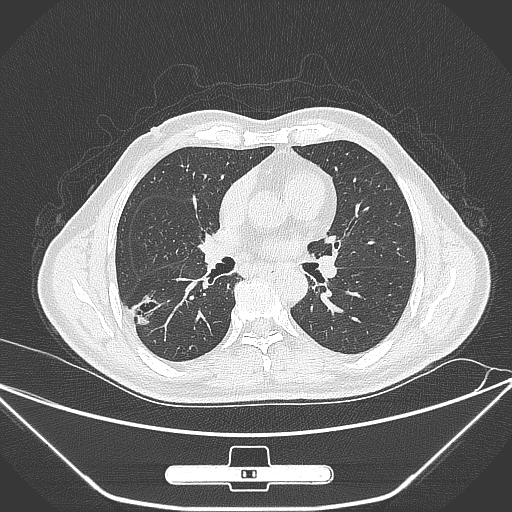
Chest CT, one axial slice; position 151 of 310 along the scan axis; lung window (W 1500 / L -600 HU); 1 mm slice thickness; 512 × 512 image matrix, field of view 398 × 398 mm. Patient: male, 71 years. Case-level facts recorded for this patient, not image findings: clinical TNM (as recorded): T1c N0 M0.
Structures marked on this image (bounding box drawn by a radiologist):
- lung tumour (recorded histology: adenocarcinoma): bounding box [x1, y1, x2, y2] px = [130, 289, 177, 332]